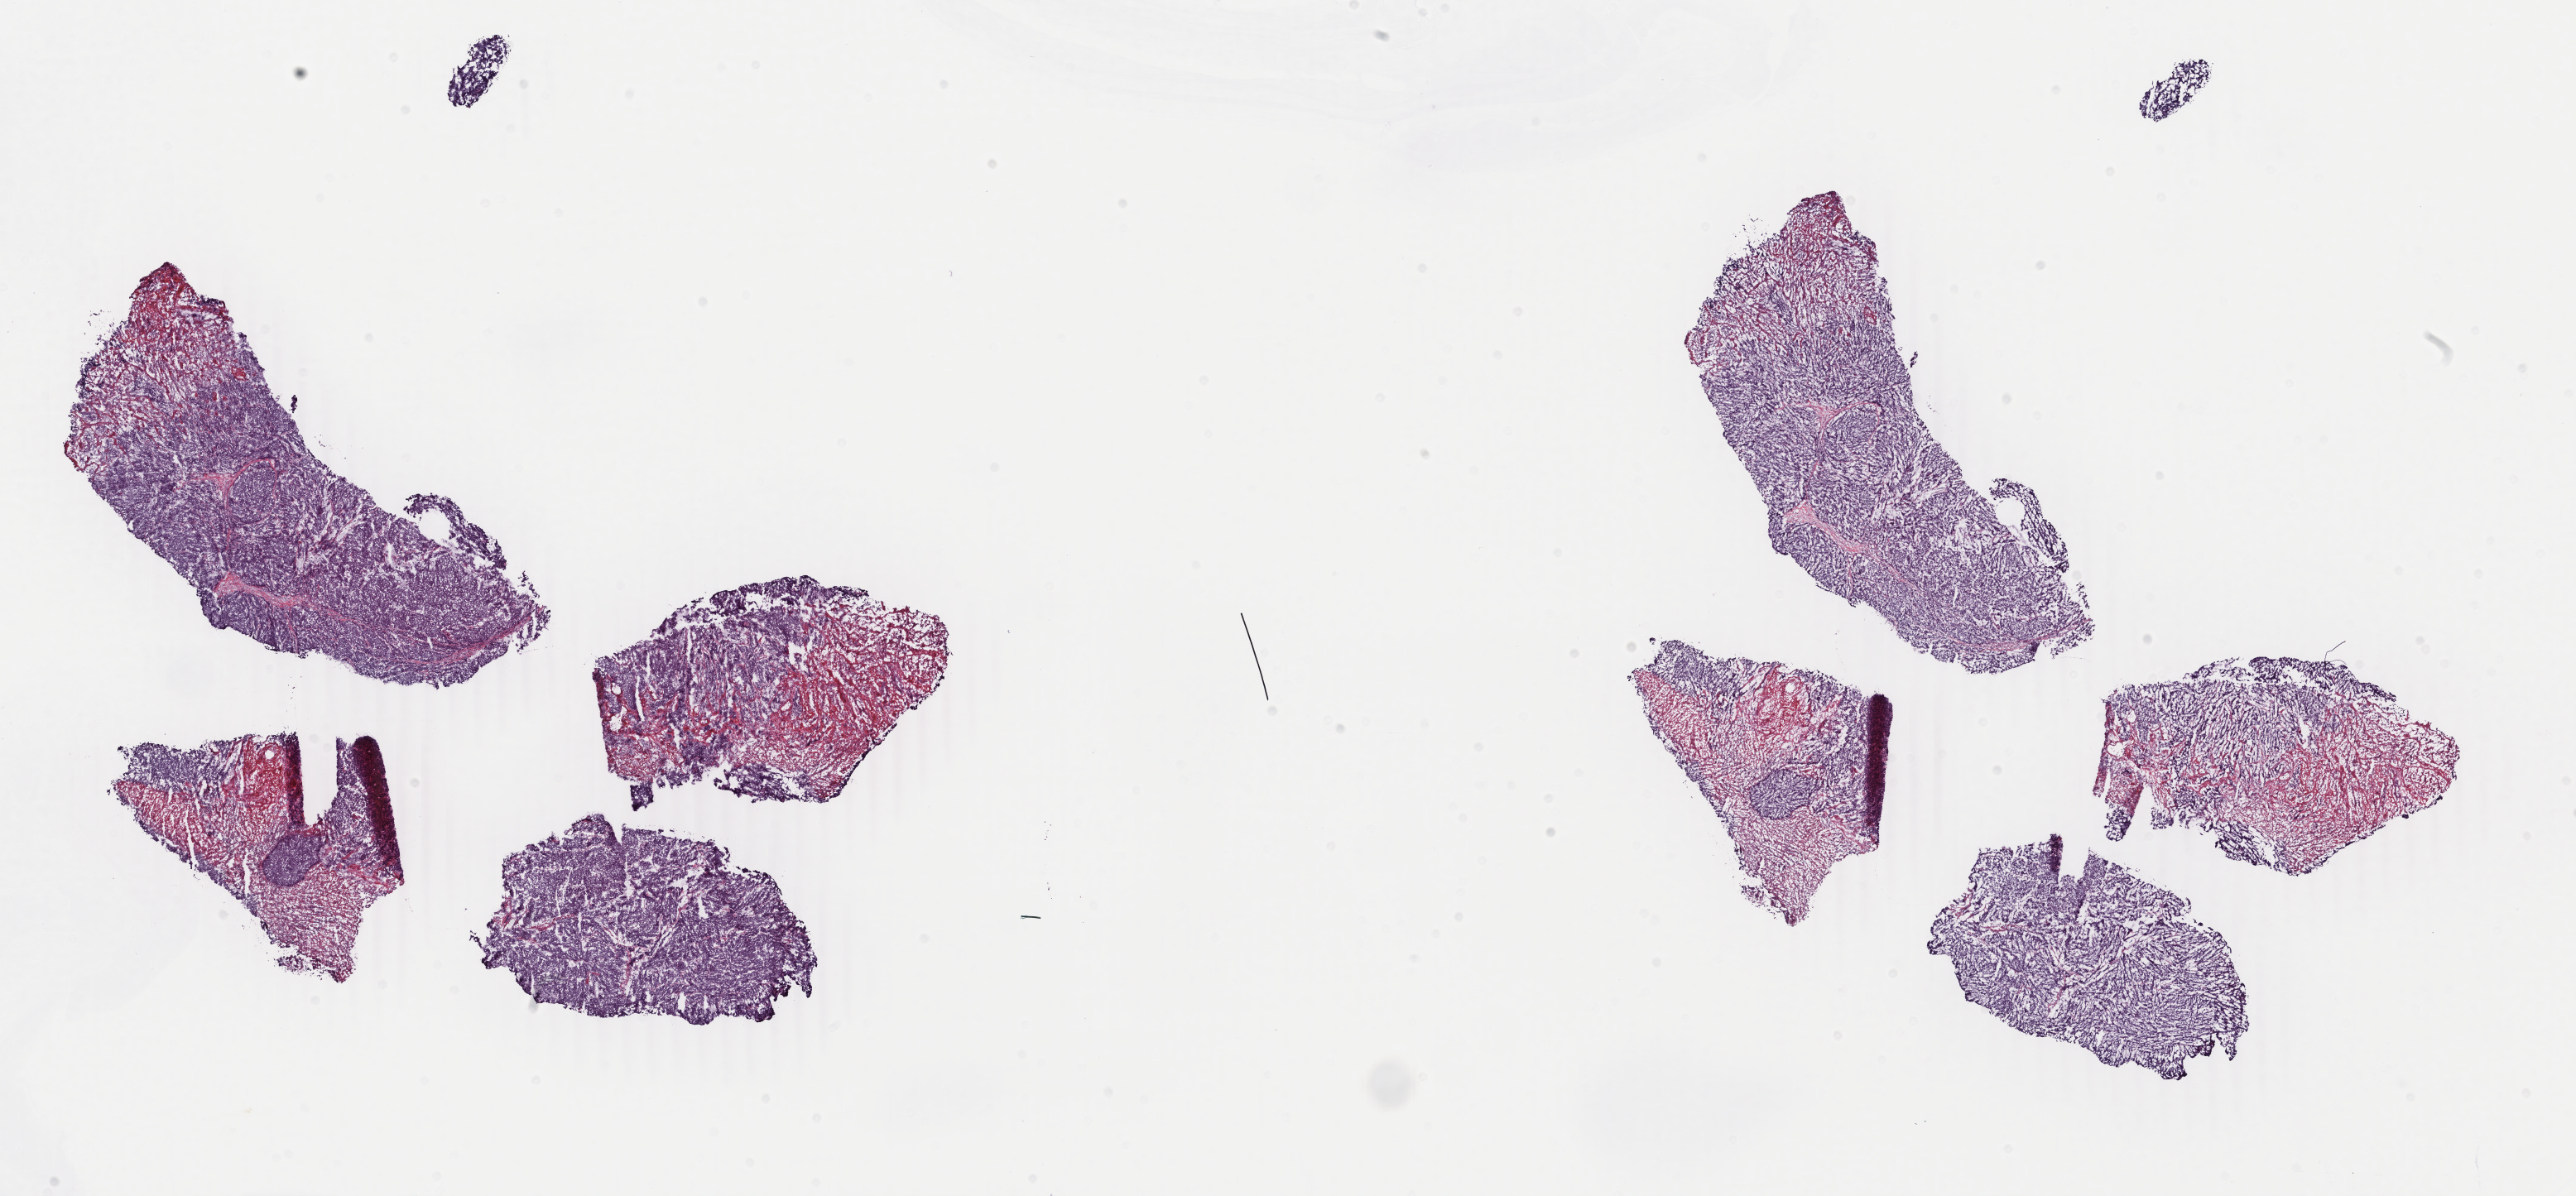
Whole-slide histology image, H&E-stained — shown as a low-resolution overview of the whole scanned area (about 24.7 x 11.5 mm). Frozen section from the top of the tissue portion. Head and neck, primary tumour sample. Male patient; age at initial diagnosis 56 years.
Histologic diagnosis: Squamous cell carcinoma, NOS (tonsil, NOS).